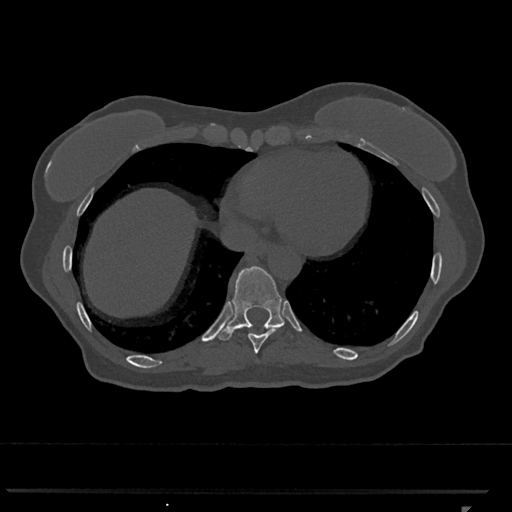
CT including the spine, one axial slice. Position 590 of 793 along the scan axis. Bone window (W 1800 / L 400 HU). 0.5 mm slice thickness. 512 × 512 image matrix, field of view 380 × 380 mm. Patient: female, 62 years. From the clinical record (not read from this slice): primary cancer: renal.
Outlined on this slice (semi-automatically segmented with operator editing):
- T10 vertebra: bounding box [x1, y1, x2, y2] px = [219, 266, 292, 341]
- T9 vertebra: [248, 326, 292, 354]